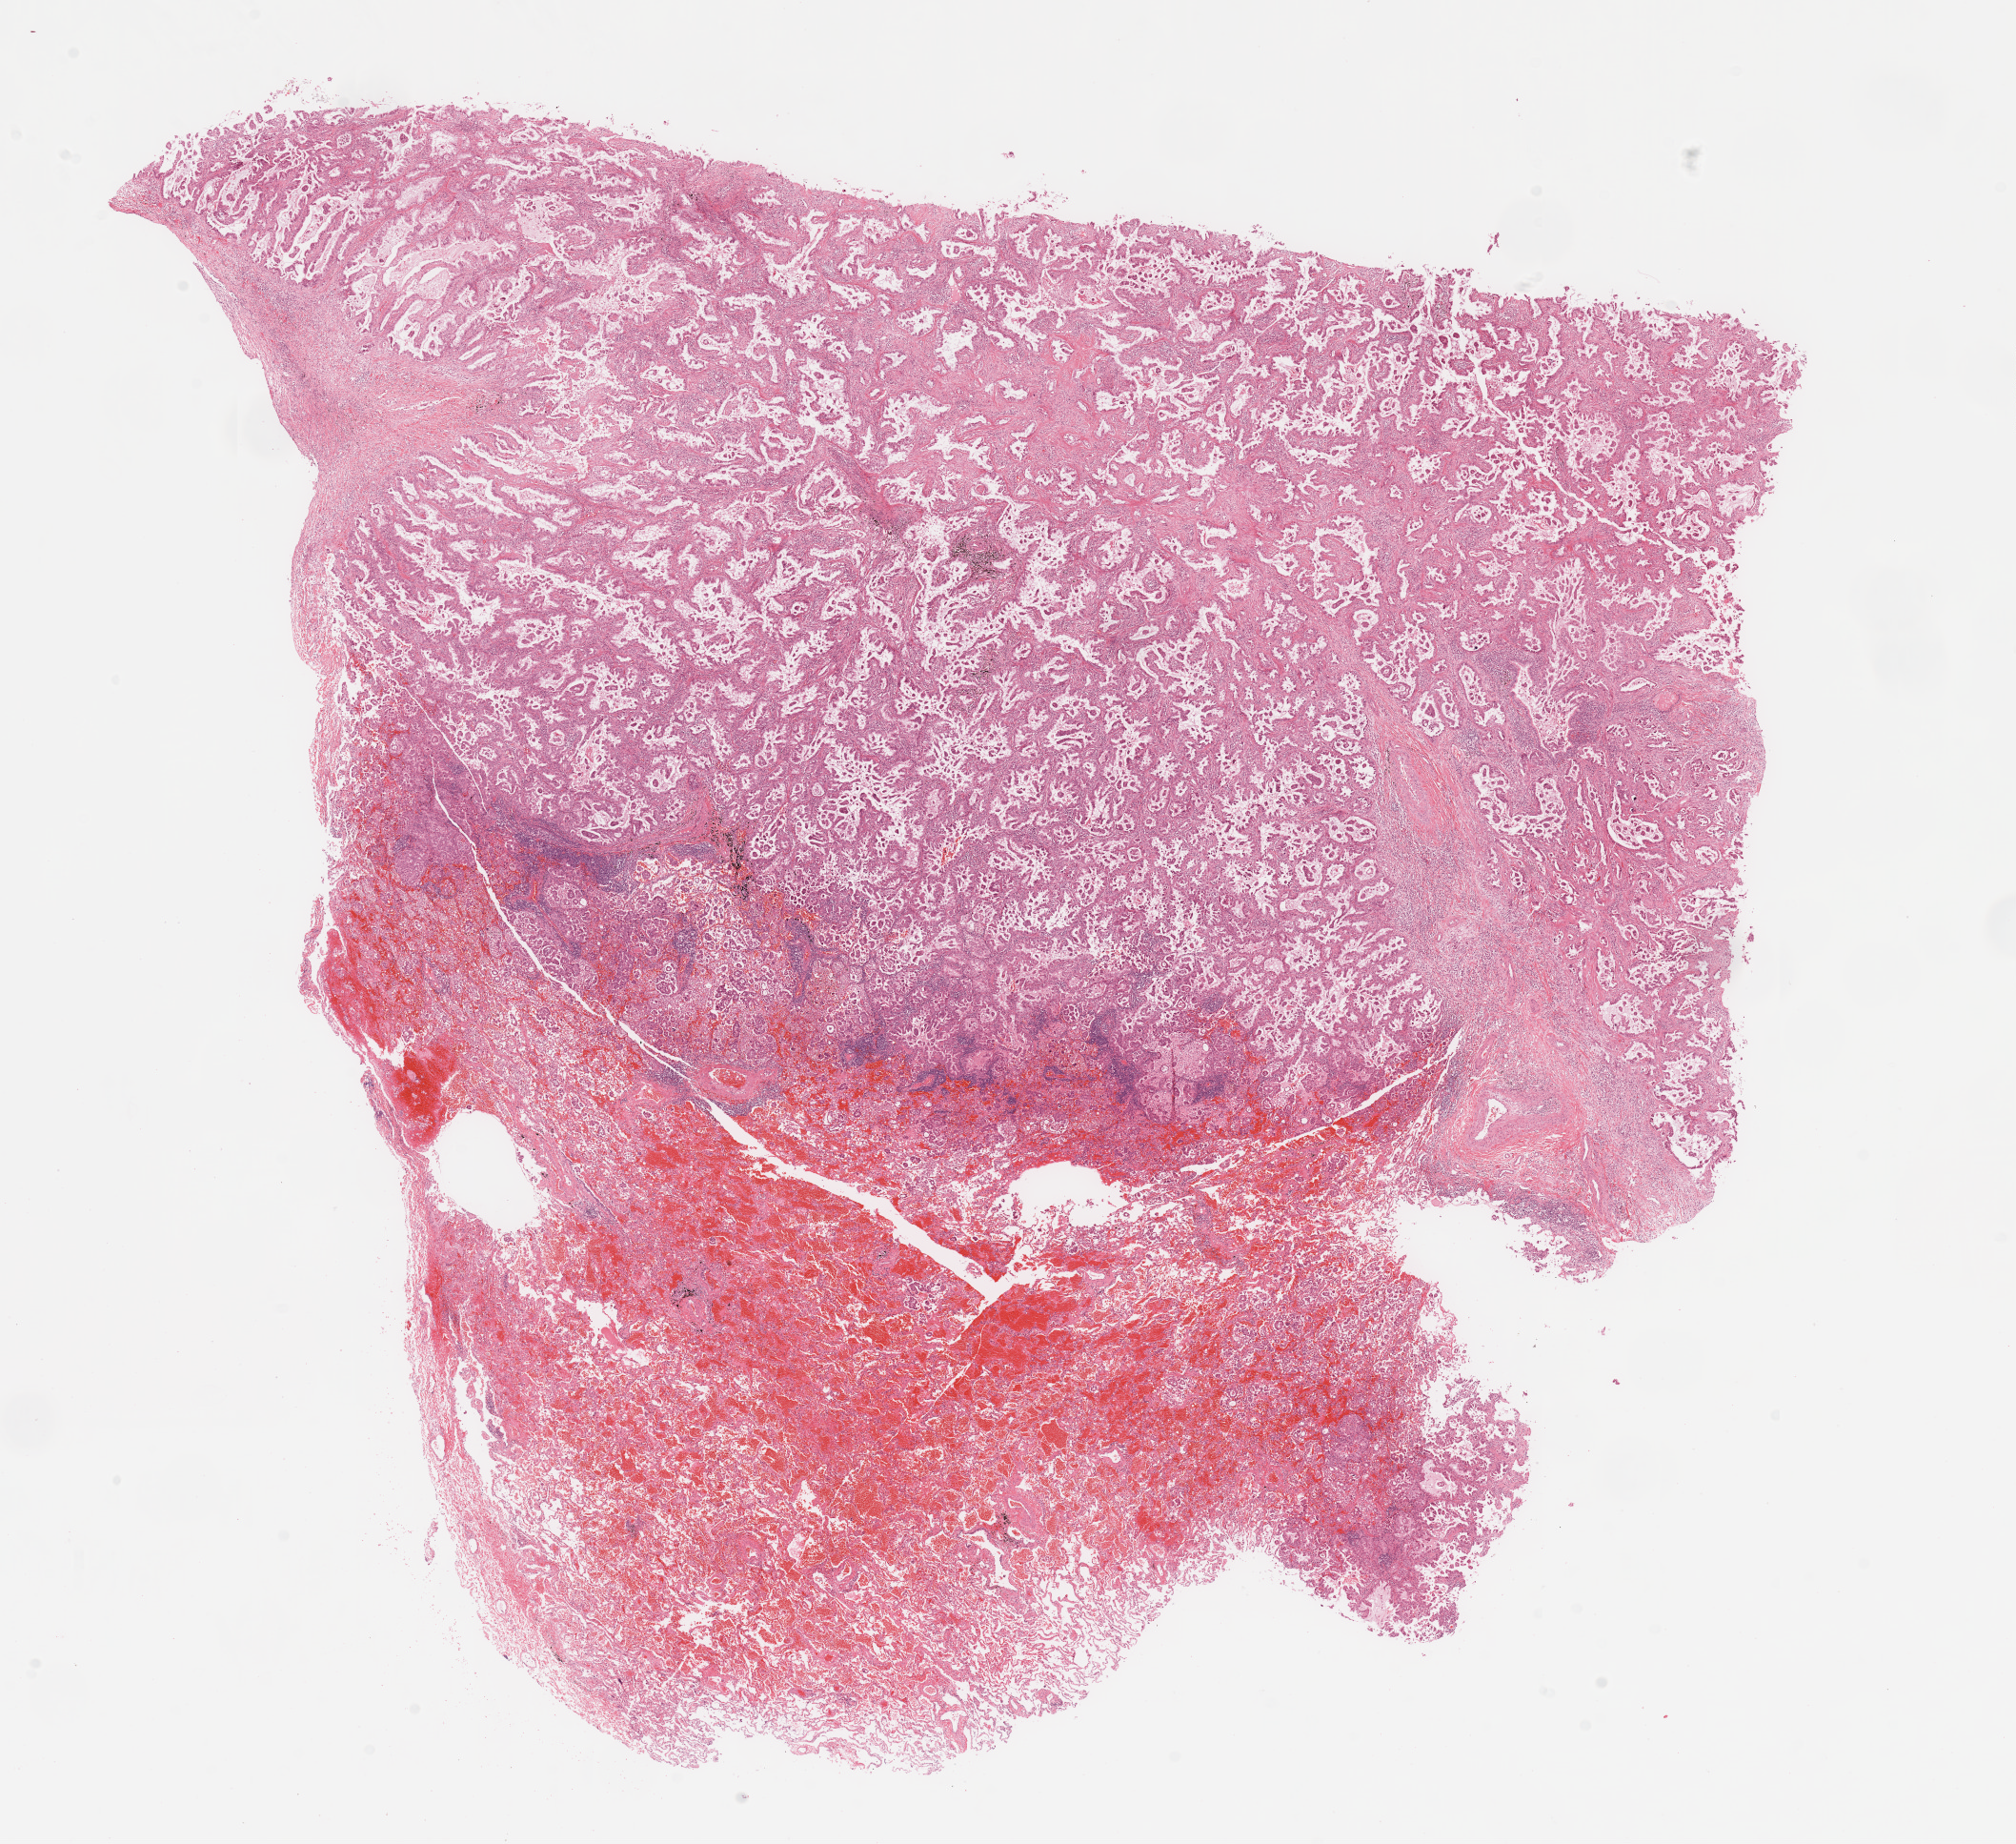
Whole-slide histology image, Hematoxylin and eosin (H&E) stained, a low-resolution overview of the entire scanned area, about 16.7 x 15.3 mm (acquisition: 20x scan); tumour tissue sample, sampled site: lung. 48-year-old female patient. Histologic grade: G2 (moderately differentiated). Composition of this section per pathologist review: tumour nuclei 70%, necrosis 10%.
Histologic diagnosis: Adenocarcinoma, NOS. AJCC pathologic stage: IA. Primary tumour site (as recorded): right lower lobe.